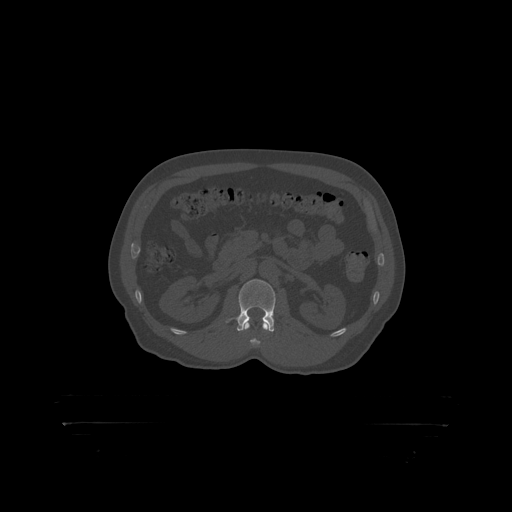
CT including the spine, one axial slice; 120 kVp; bone window (W 1800 / L 400 HU); 1.25 mm slice thickness; 512 × 512 image matrix. Patient: male, 46 years. Case-level facts recorded for this patient, not image findings: primary cancer: skin.
Annotated regions visible in this slice (semi-automatic segmentation, software-assisted and operator-edited):
- L2 vertebra: bounding box [x1, y1, x2, y2] px = [239, 280, 276, 319]